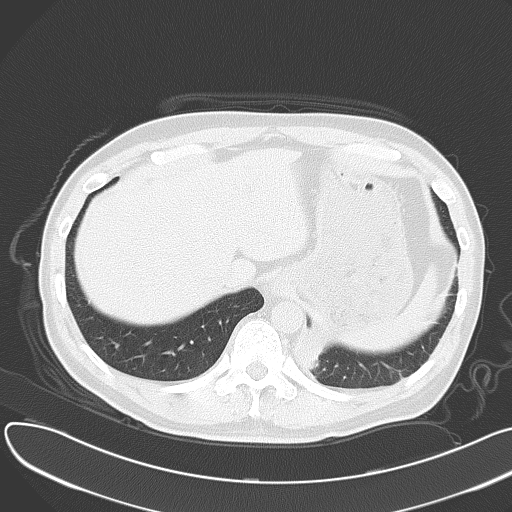
Chest CT, one axial slice. Slice 7 of 55 in the series (ordered by position). 120 kVp. Lung window (W 1500 / L -600 HU). 512 × 512 image matrix, field of view 376 × 376 mm. Male patient, age 55 years. Case-level facts recorded for this patient, not image findings: clinical TNM (as recorded): T2 N3 M0; histopathological grade: G3.
Annotated regions visible in this slice (bounding box drawn by a radiologist):
- lung tumour (recorded histology: small cell carcinoma): box from (x=301, y=322) to (x=328, y=379) px